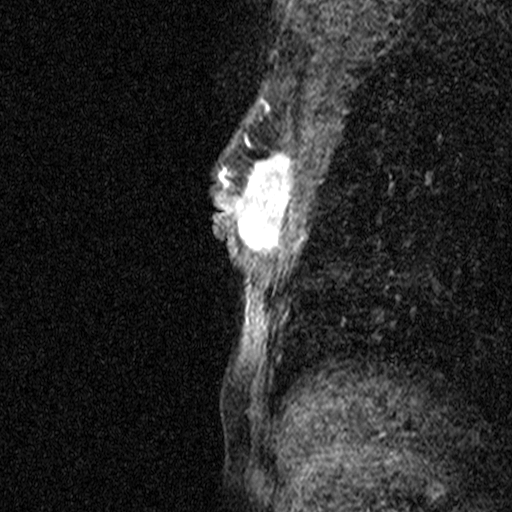
Breast MRI (dynamic contrast-enhanced), one sagittal slice. Slice 26 of 44 in the series (ordered by position). Dynamic contrast-enhanced study with each time point stored as its own series, time point 2 of 3 at this slice position (early post-contrast, ordered by acquisition time). 1.5 T. TE 4.5 ms, TR 11 ms. 3 mm slice thickness. 512 × 512 image matrix, field of view 200 × 200 mm. Patient: female, 44 years. From the clinical record (not read from this slice): setting: breast cancer imaged before/during neoadjuvant chemotherapy; receptor status: HR-positive, HER2-negative.
Outlined on this slice (semi-automatically segmented with operator editing):
- analysis volume of interest (the breast-tissue region the enhancement analysis was run in; not a lesion): bounding box (x1, y1, x2, y2) in pixels: (218, 118, 288, 291)
- tumour enhancement mask (voxels above the 90 % enhancement threshold inside the analysis volume of interest): (220, 135, 288, 249)